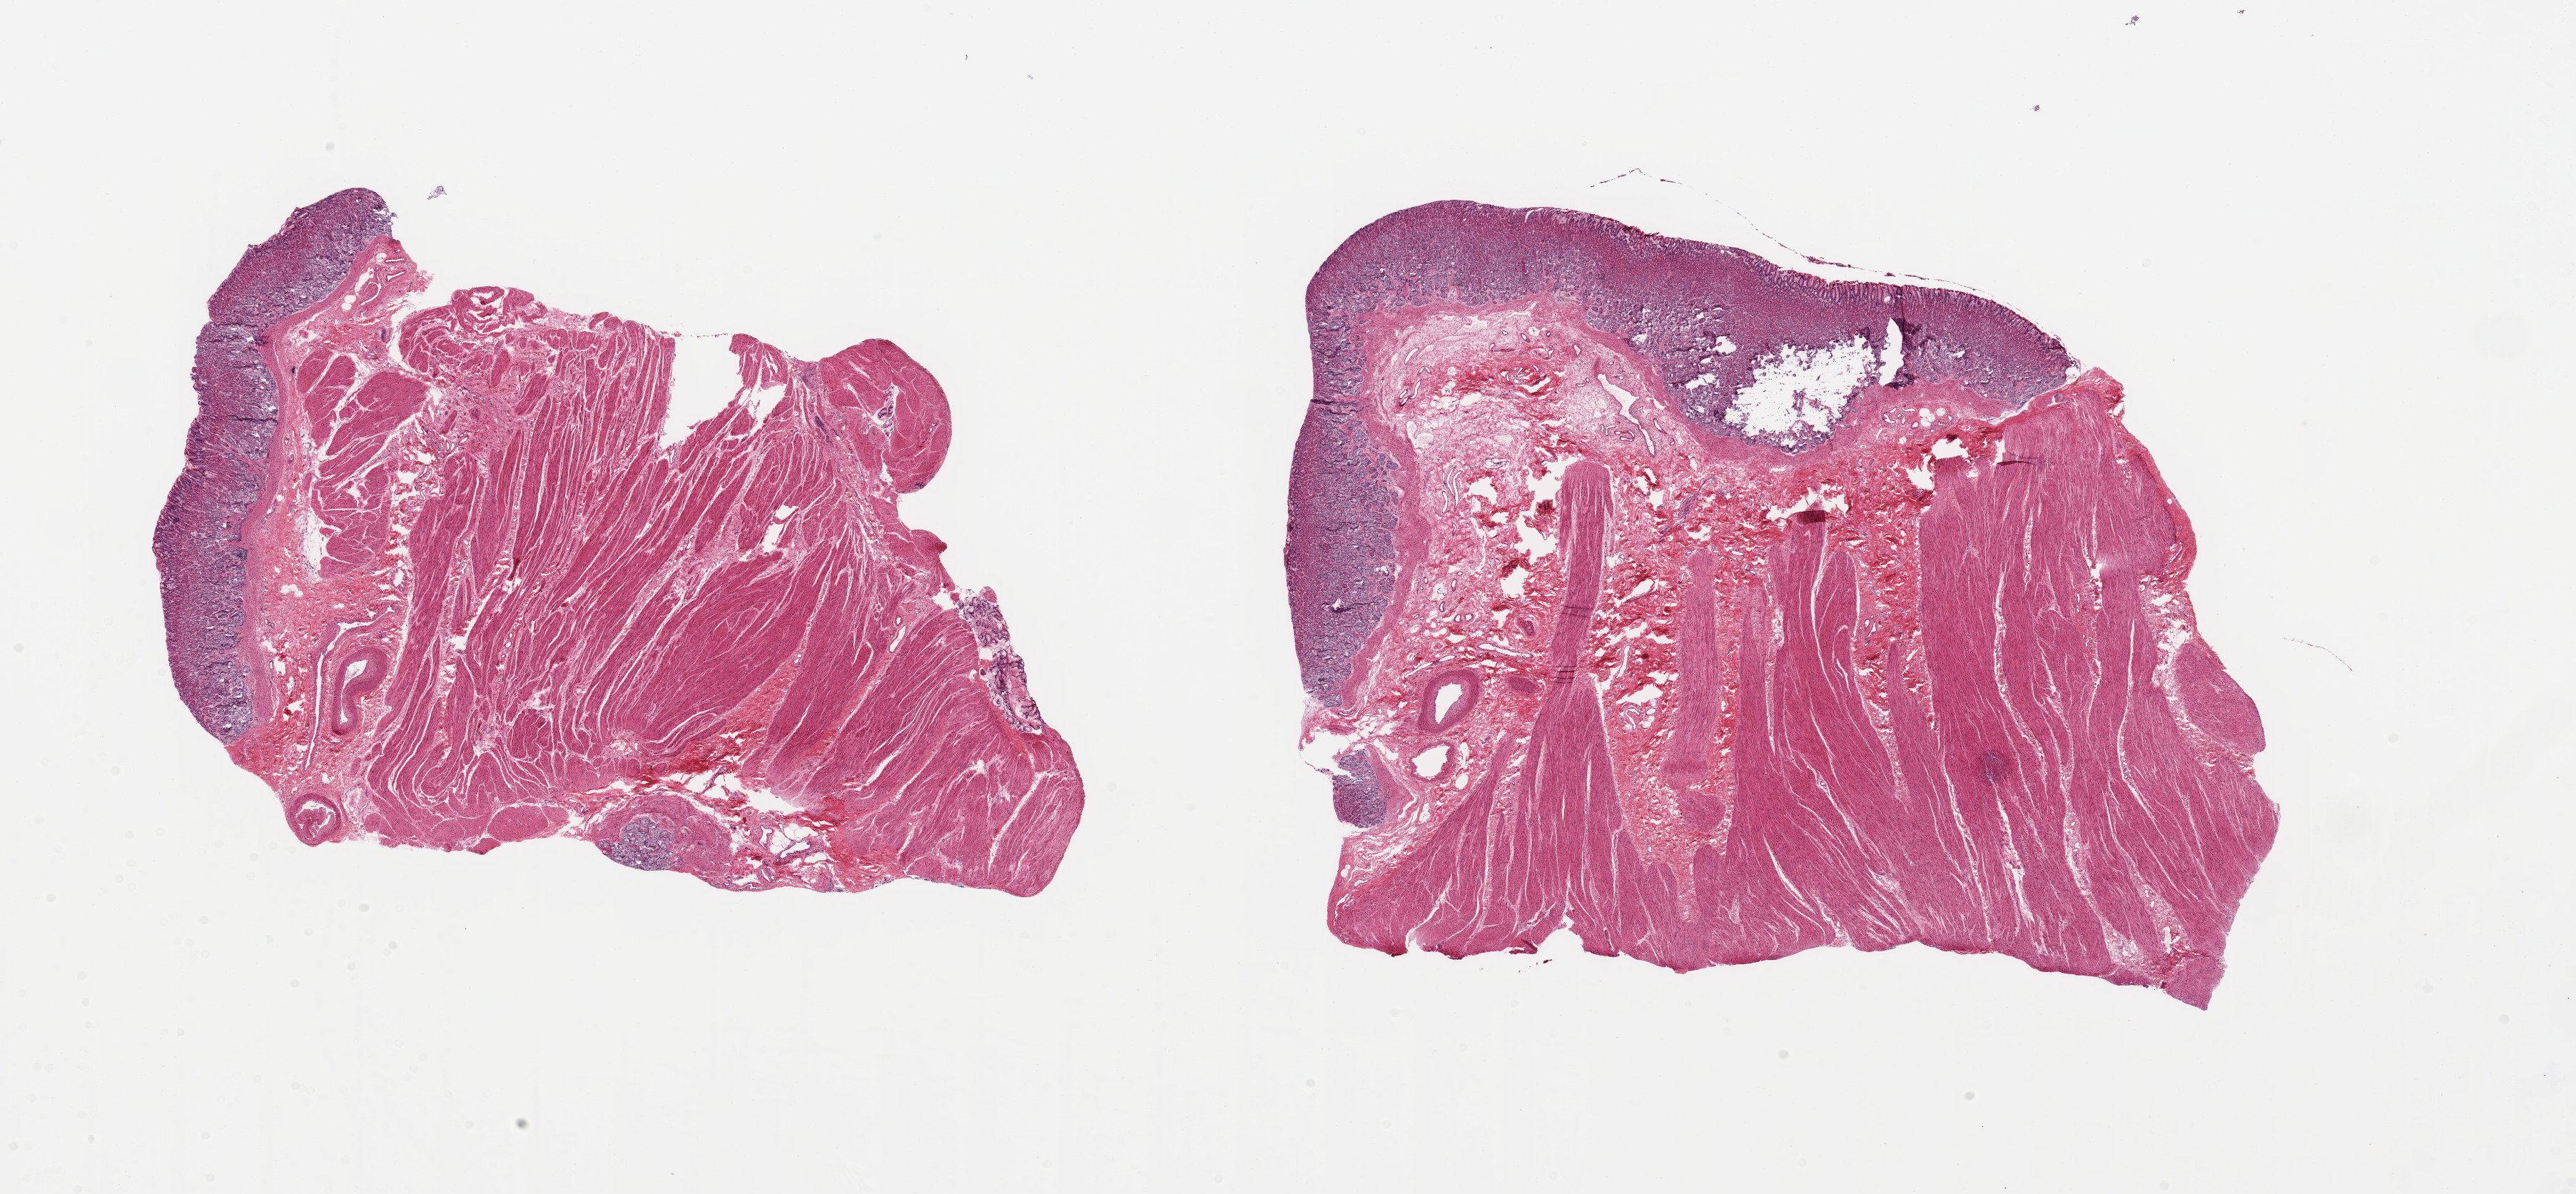
Digitized hematoxylin and eosin (H&E)-stained section, low-resolution overview of the scanned area, about 28.5 x 13.2 mm; PAXgene-fixed, paraffin-embedded tissue; target tissue: stomach; tissue donor sample. Female donor.
Review note (as recorded): 2 pieces. Mucosa extremely well-preserved, ~10 of thickness. Focal poor fixation with tears.